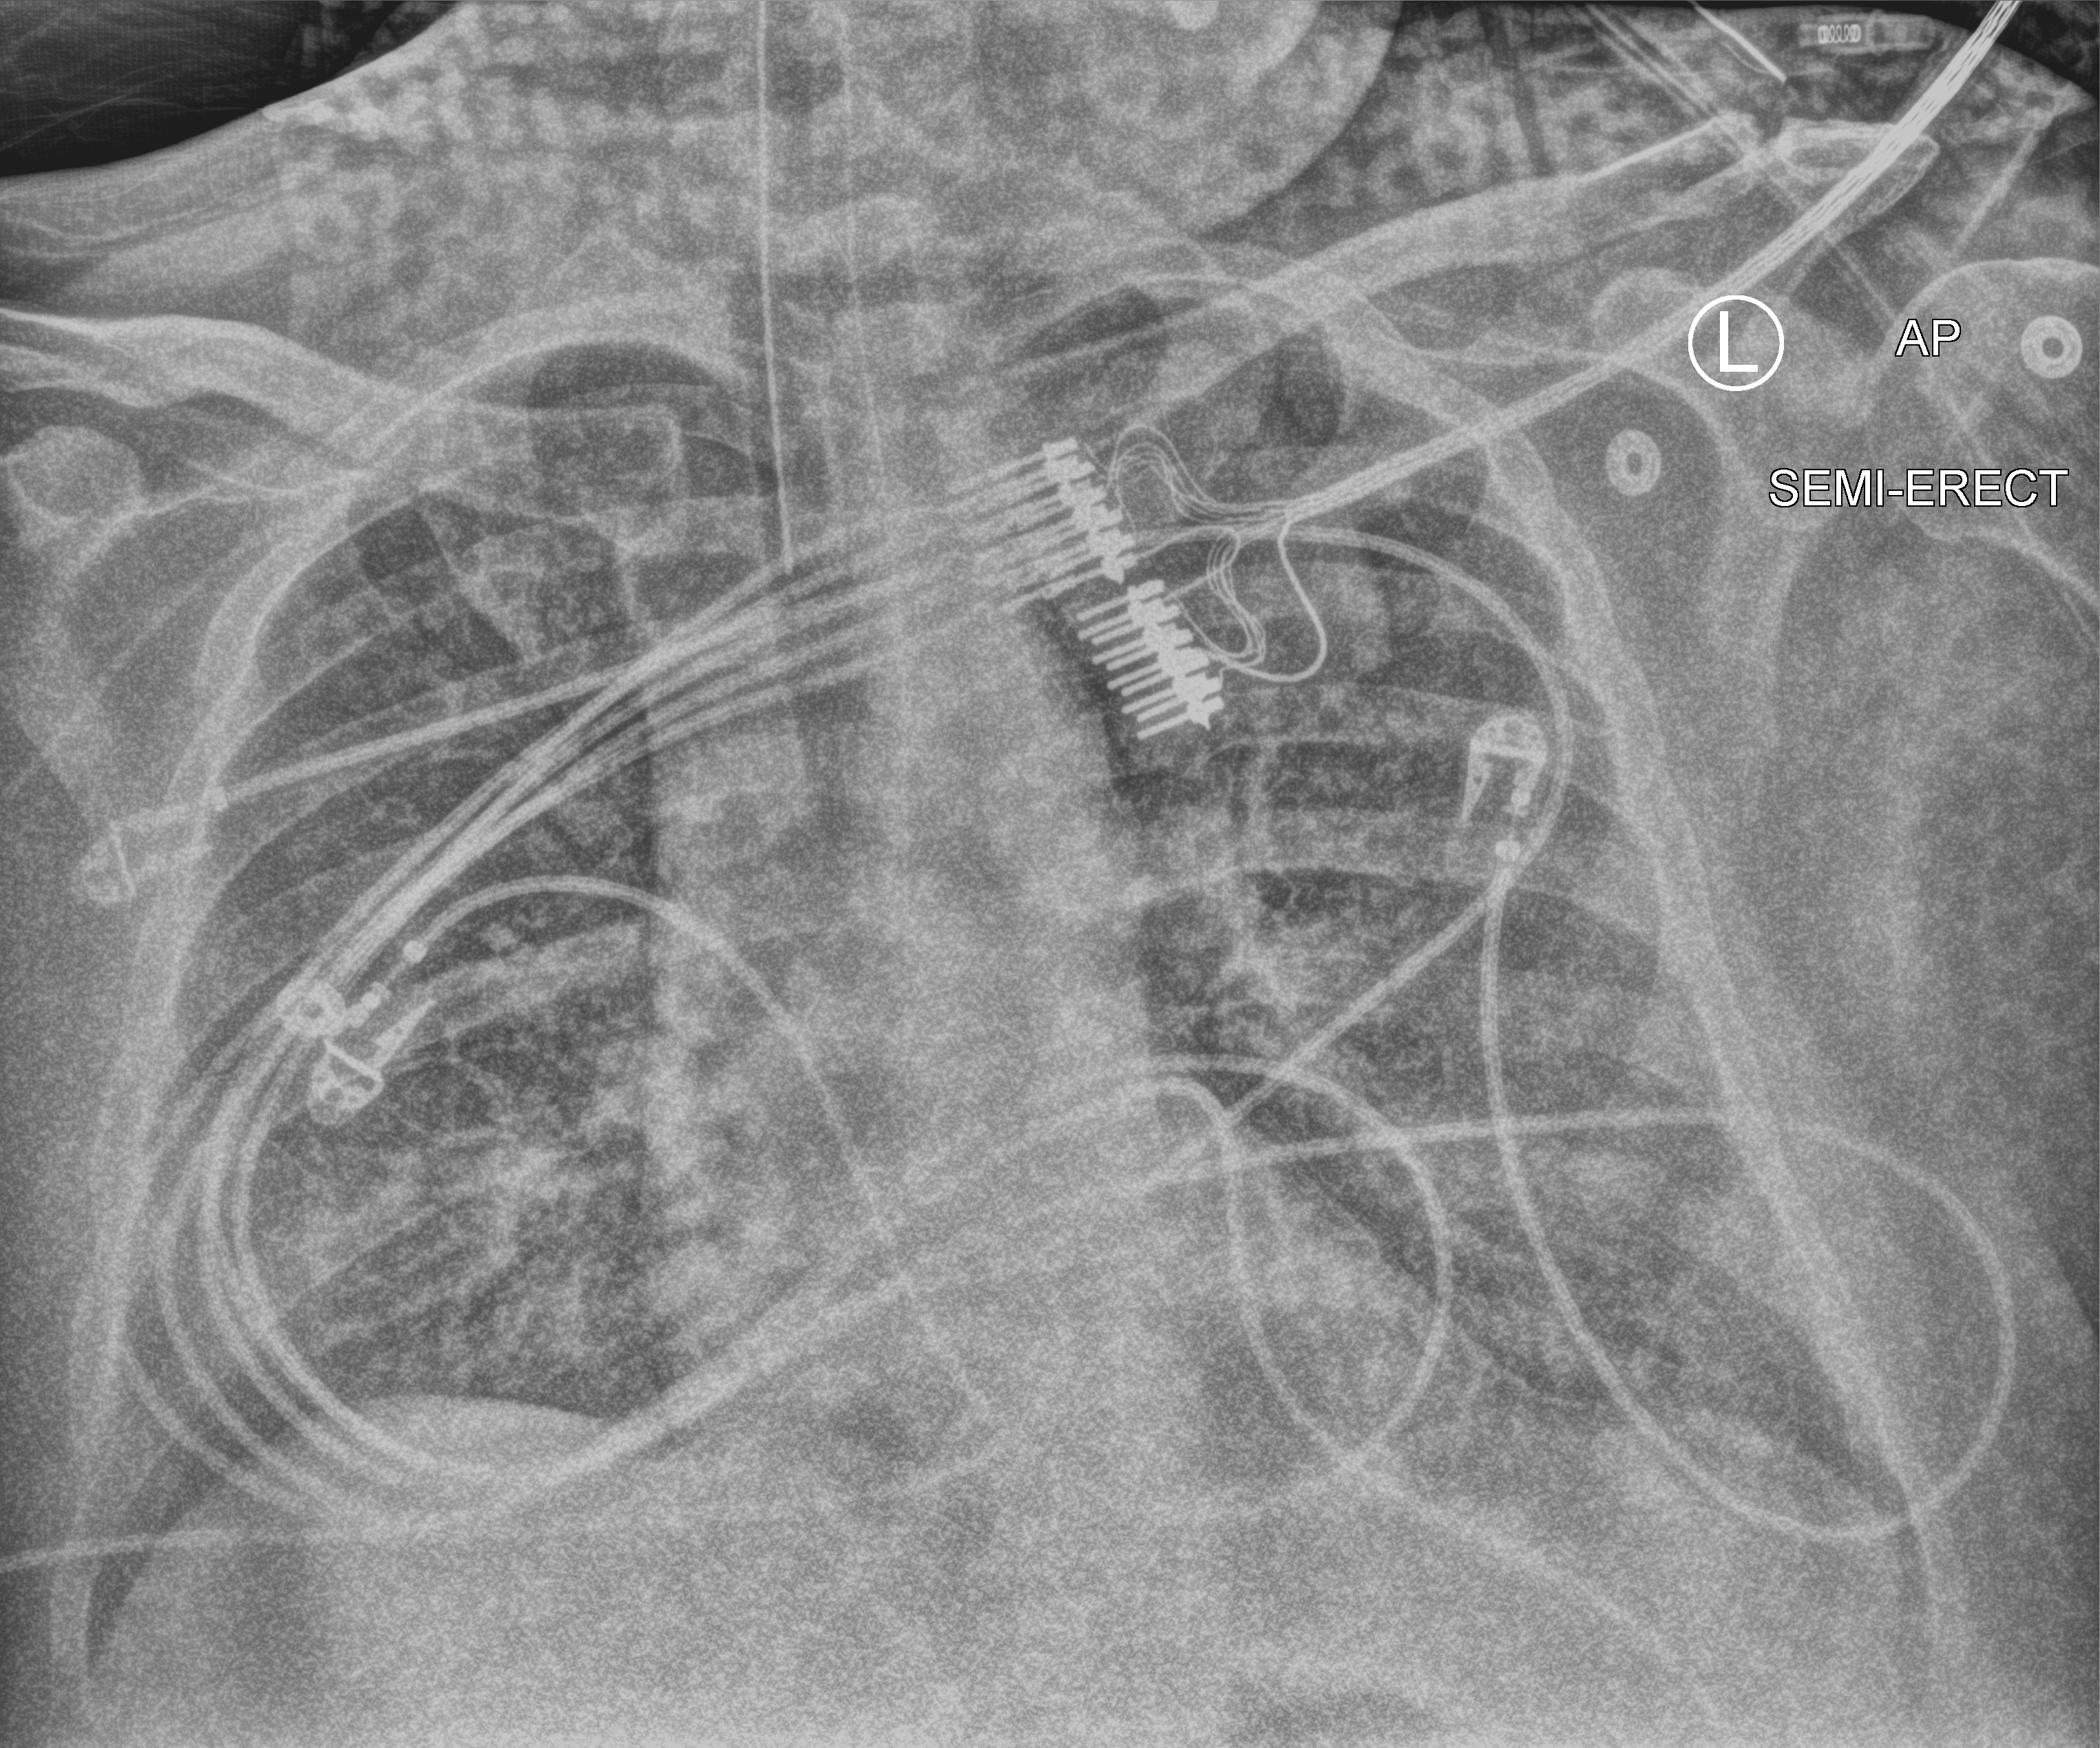
Bedside chest radiograph (computed radiography), anteroposterior (AP) projection. Adult patient hospitalised with COVID-19, age 18–59 years.
Hospital-stay facts (about this admission, not read from this image; timing relative to this image not recorded):
- smoking status (admission record): never